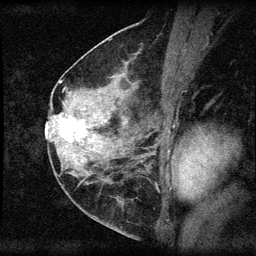
Breast MRI (dynamic contrast-enhanced), one sagittal slice; slice 29 of 60 in the series (ordered by position); dynamic contrast-enhanced series, image 2 of 3 at this slice position (ordered by acquisition); 1.5 T; TE 4.2 ms, TR 8.2 ms; 2 mm slice thickness; 256 × 256 image matrix, field of view 180 × 180 mm. Patient: female, 45 years.
Outlined on this slice (semi-automatically segmented with operator editing):
- analysis volume of interest (the breast-tissue region the enhancement analysis was run in; not a lesion): bounding box [x1, y1, x2, y2] px = [55, 110, 94, 148]
- tumour enhancement mask (voxels above the 70 % enhancement threshold inside the analysis volume of interest): [60, 117, 86, 143]